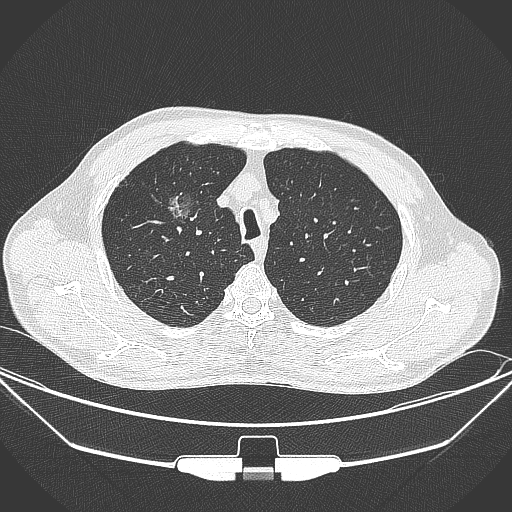
Chest CT, one axial slice; position 273 of 355 along the scan axis; 120 kVp; lung window (W 1500 / L -600 HU); 1 mm slice thickness; 512 × 512 image matrix, field of view 399 × 399 mm. Male patient, age 67 years. Case-level facts recorded for this patient, not image findings: clinical TNM (as recorded): T1c N0 M0; histopathological grade: G2.
Annotated regions visible in this slice (rectangle marked by the reading radiologist):
- lung tumour (recorded histology: adenocarcinoma): bounding box (x1, y1, x2, y2) in pixels: (145, 174, 204, 228)